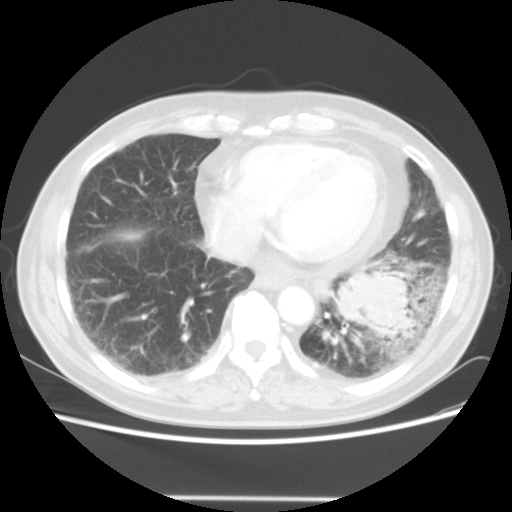
Chest CT, one axial slice; 140 kVp; lung window (W 1500 / L -600 HU); 5 mm slice thickness; 512 × 512 image matrix, field of view 360 × 360 mm. Patient: male, 66 years. Case-level facts recorded for this patient, not image findings: clinical TNM (as recorded): T4 N3 M0; histopathological grade: G3.
Outlined on this slice (bounding box drawn by a radiologist):
- lung tumour (recorded histology: small cell carcinoma): bounding box (x1, y1, x2, y2) in pixels: (328, 253, 421, 353)